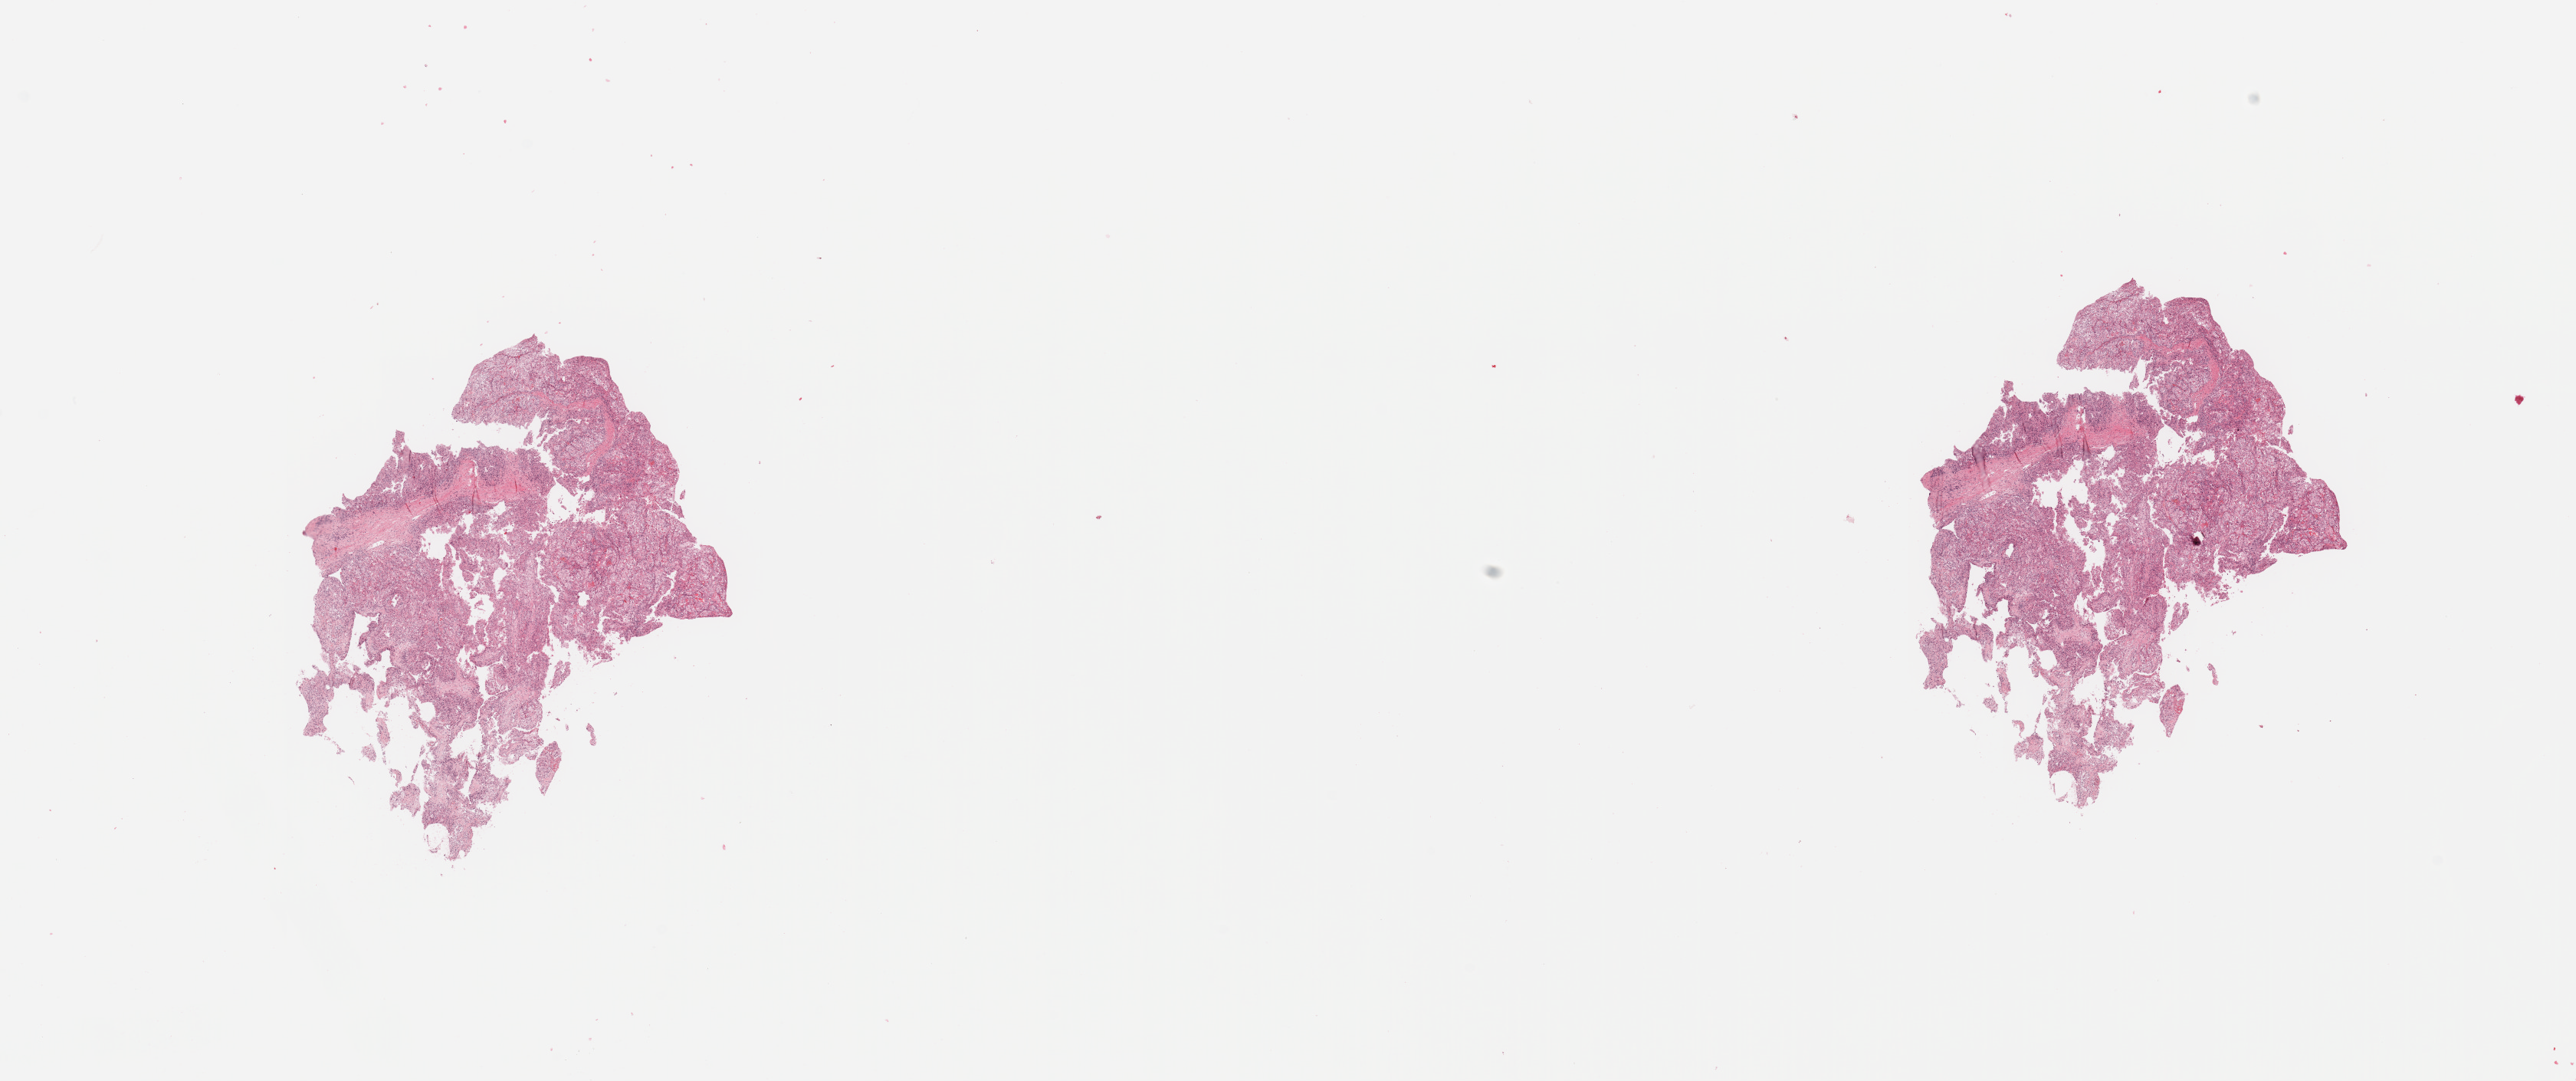
Hematoxylin and eosin (H&E) stained whole-slide image, whole scanned area (about 26.6 x 11.2 mm) shown as a low-resolution overview; tumour tissue sample, sampled site: kidney. 41-year-old male patient. Histologic grade: G3 (poorly differentiated). Composition of this section per pathologist review: tumour nuclei 90%, necrosis 5%.
Diagnosis: Renal cell carcinoma, NOS. AJCC pathologic stage: II. Primary tumour site (as recorded): upper pole.